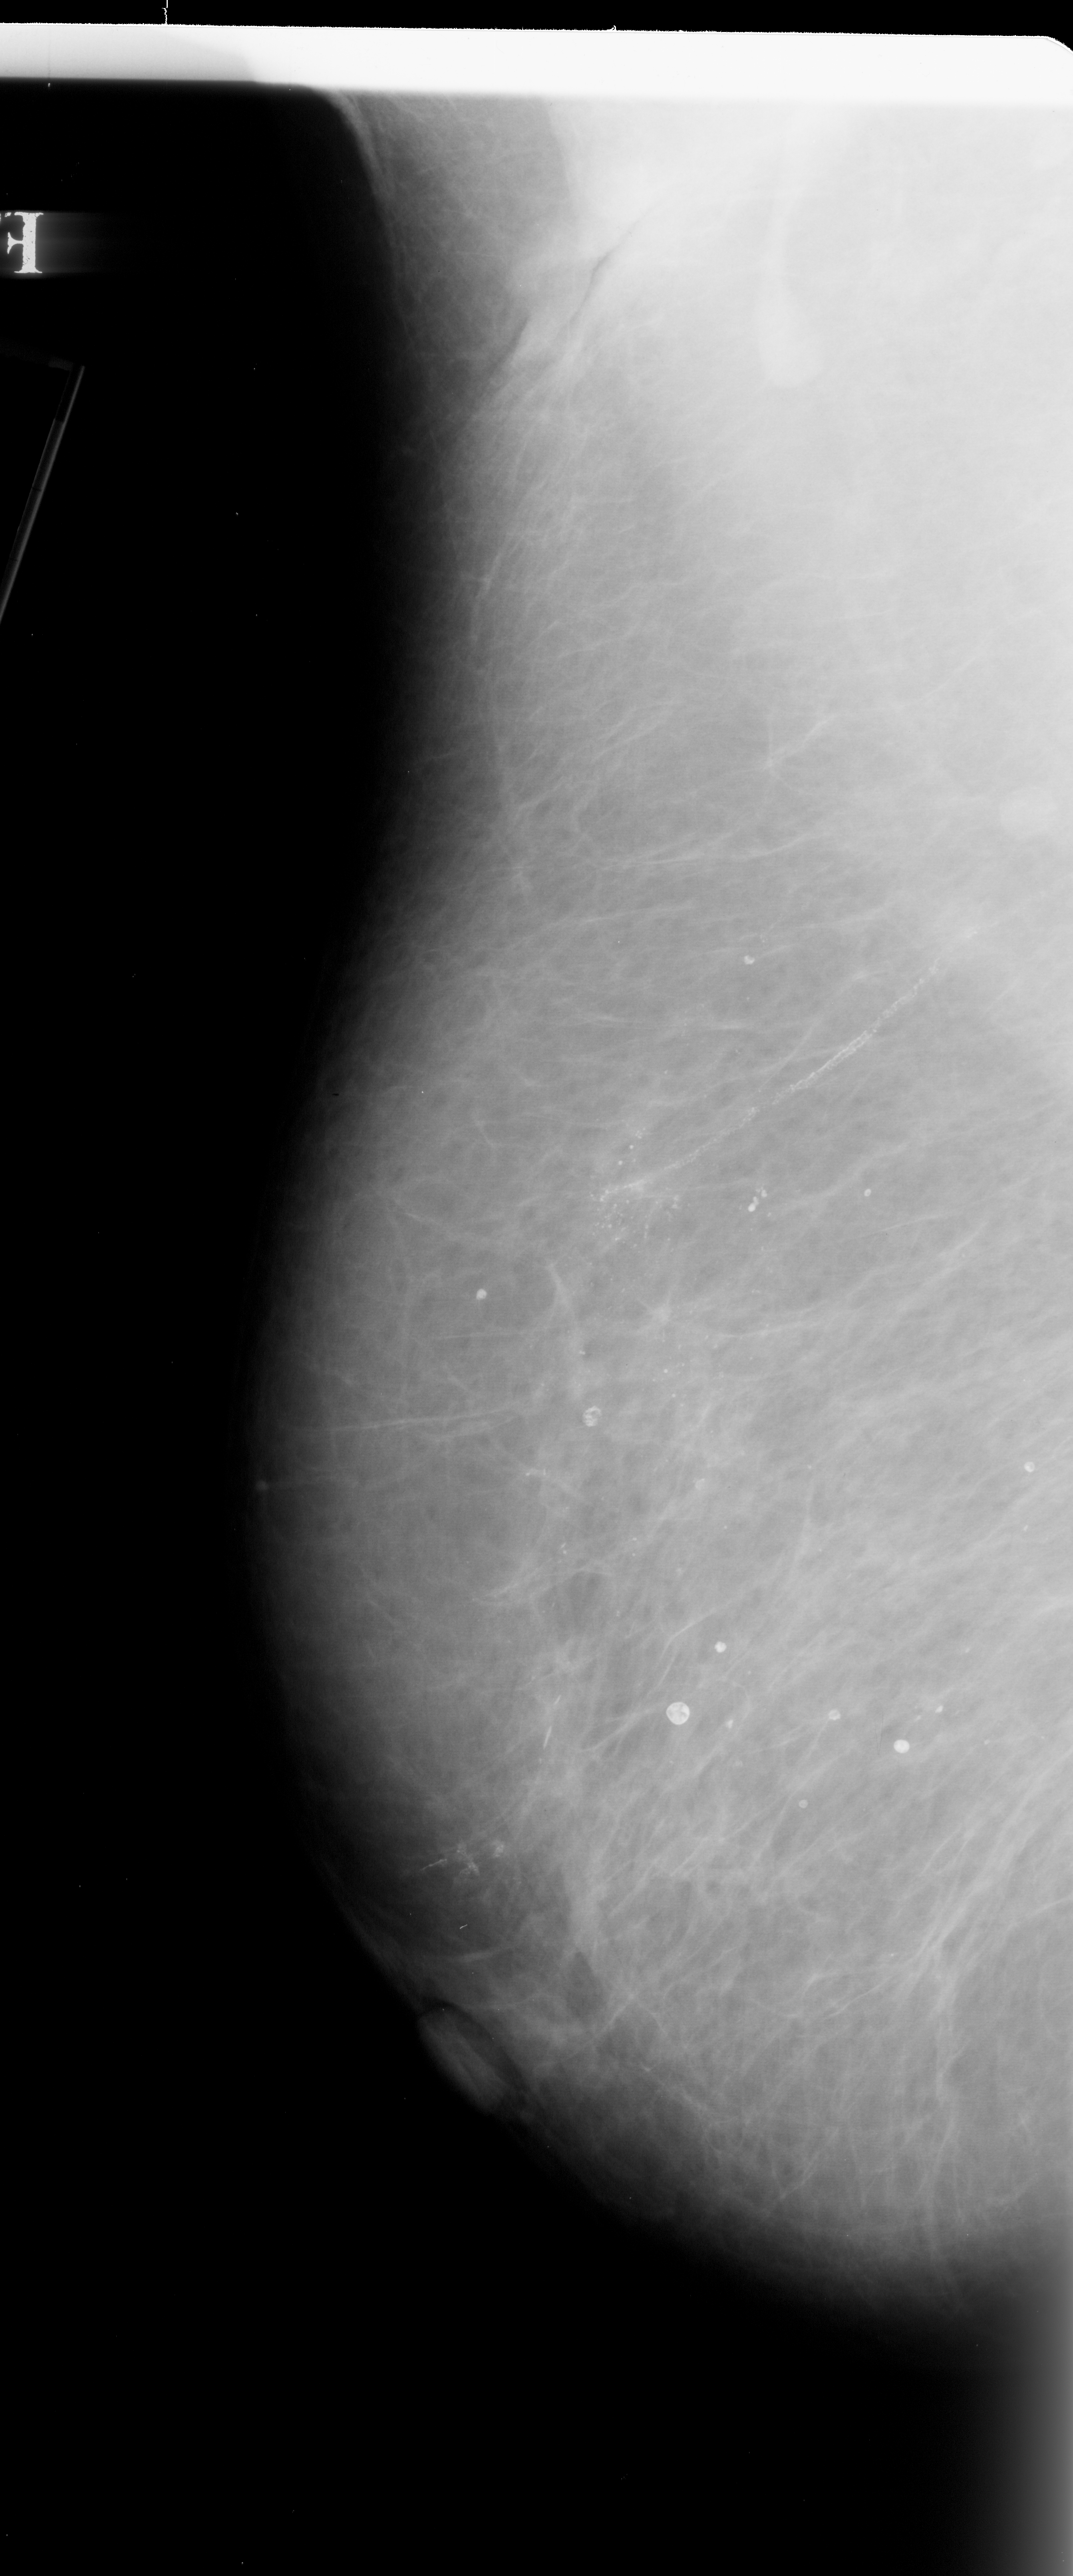
Scanned film-screen mammogram. Left breast. MLO view. Breast composition: scattered fibroglandular densities (BI-RADS density category 2 of 4). 1073 × 2576 image matrix.
Expert-marked regions of interest on this image (one box per marked abnormality):
- calcifications, morphology pleomorphic, distribution segmental; BI-RADS assessment category 4; pathology result (as recorded, not read from the image): malignant: bounding box <500,903,801,1693> (left, top, right, bottom; pixels)